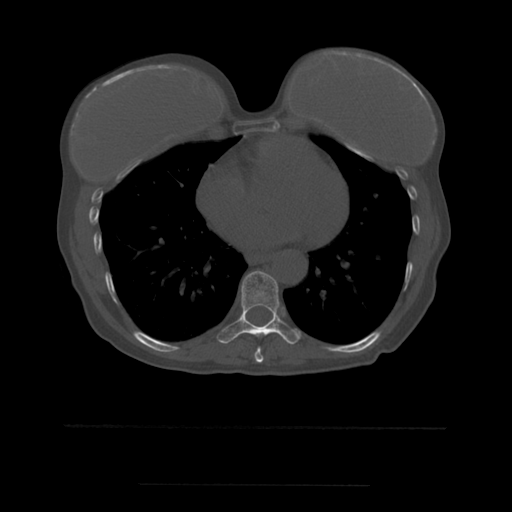
CT including the spine, one axial slice; position 324 of 544 along the scan axis; bone window (W 1800 / L 400 HU); 512 × 512 image matrix, field of view 350 × 350 mm. Patient age 58 years. Case-level facts recorded for this patient, not image findings: primary cancer: lung.
Outlined on this slice (semi-automatically segmented with operator editing):
- T8 vertebra: bounding box (x1, y1, x2, y2) in pixels: (255, 347, 264, 363)
- T9 vertebra: (218, 271, 302, 345)